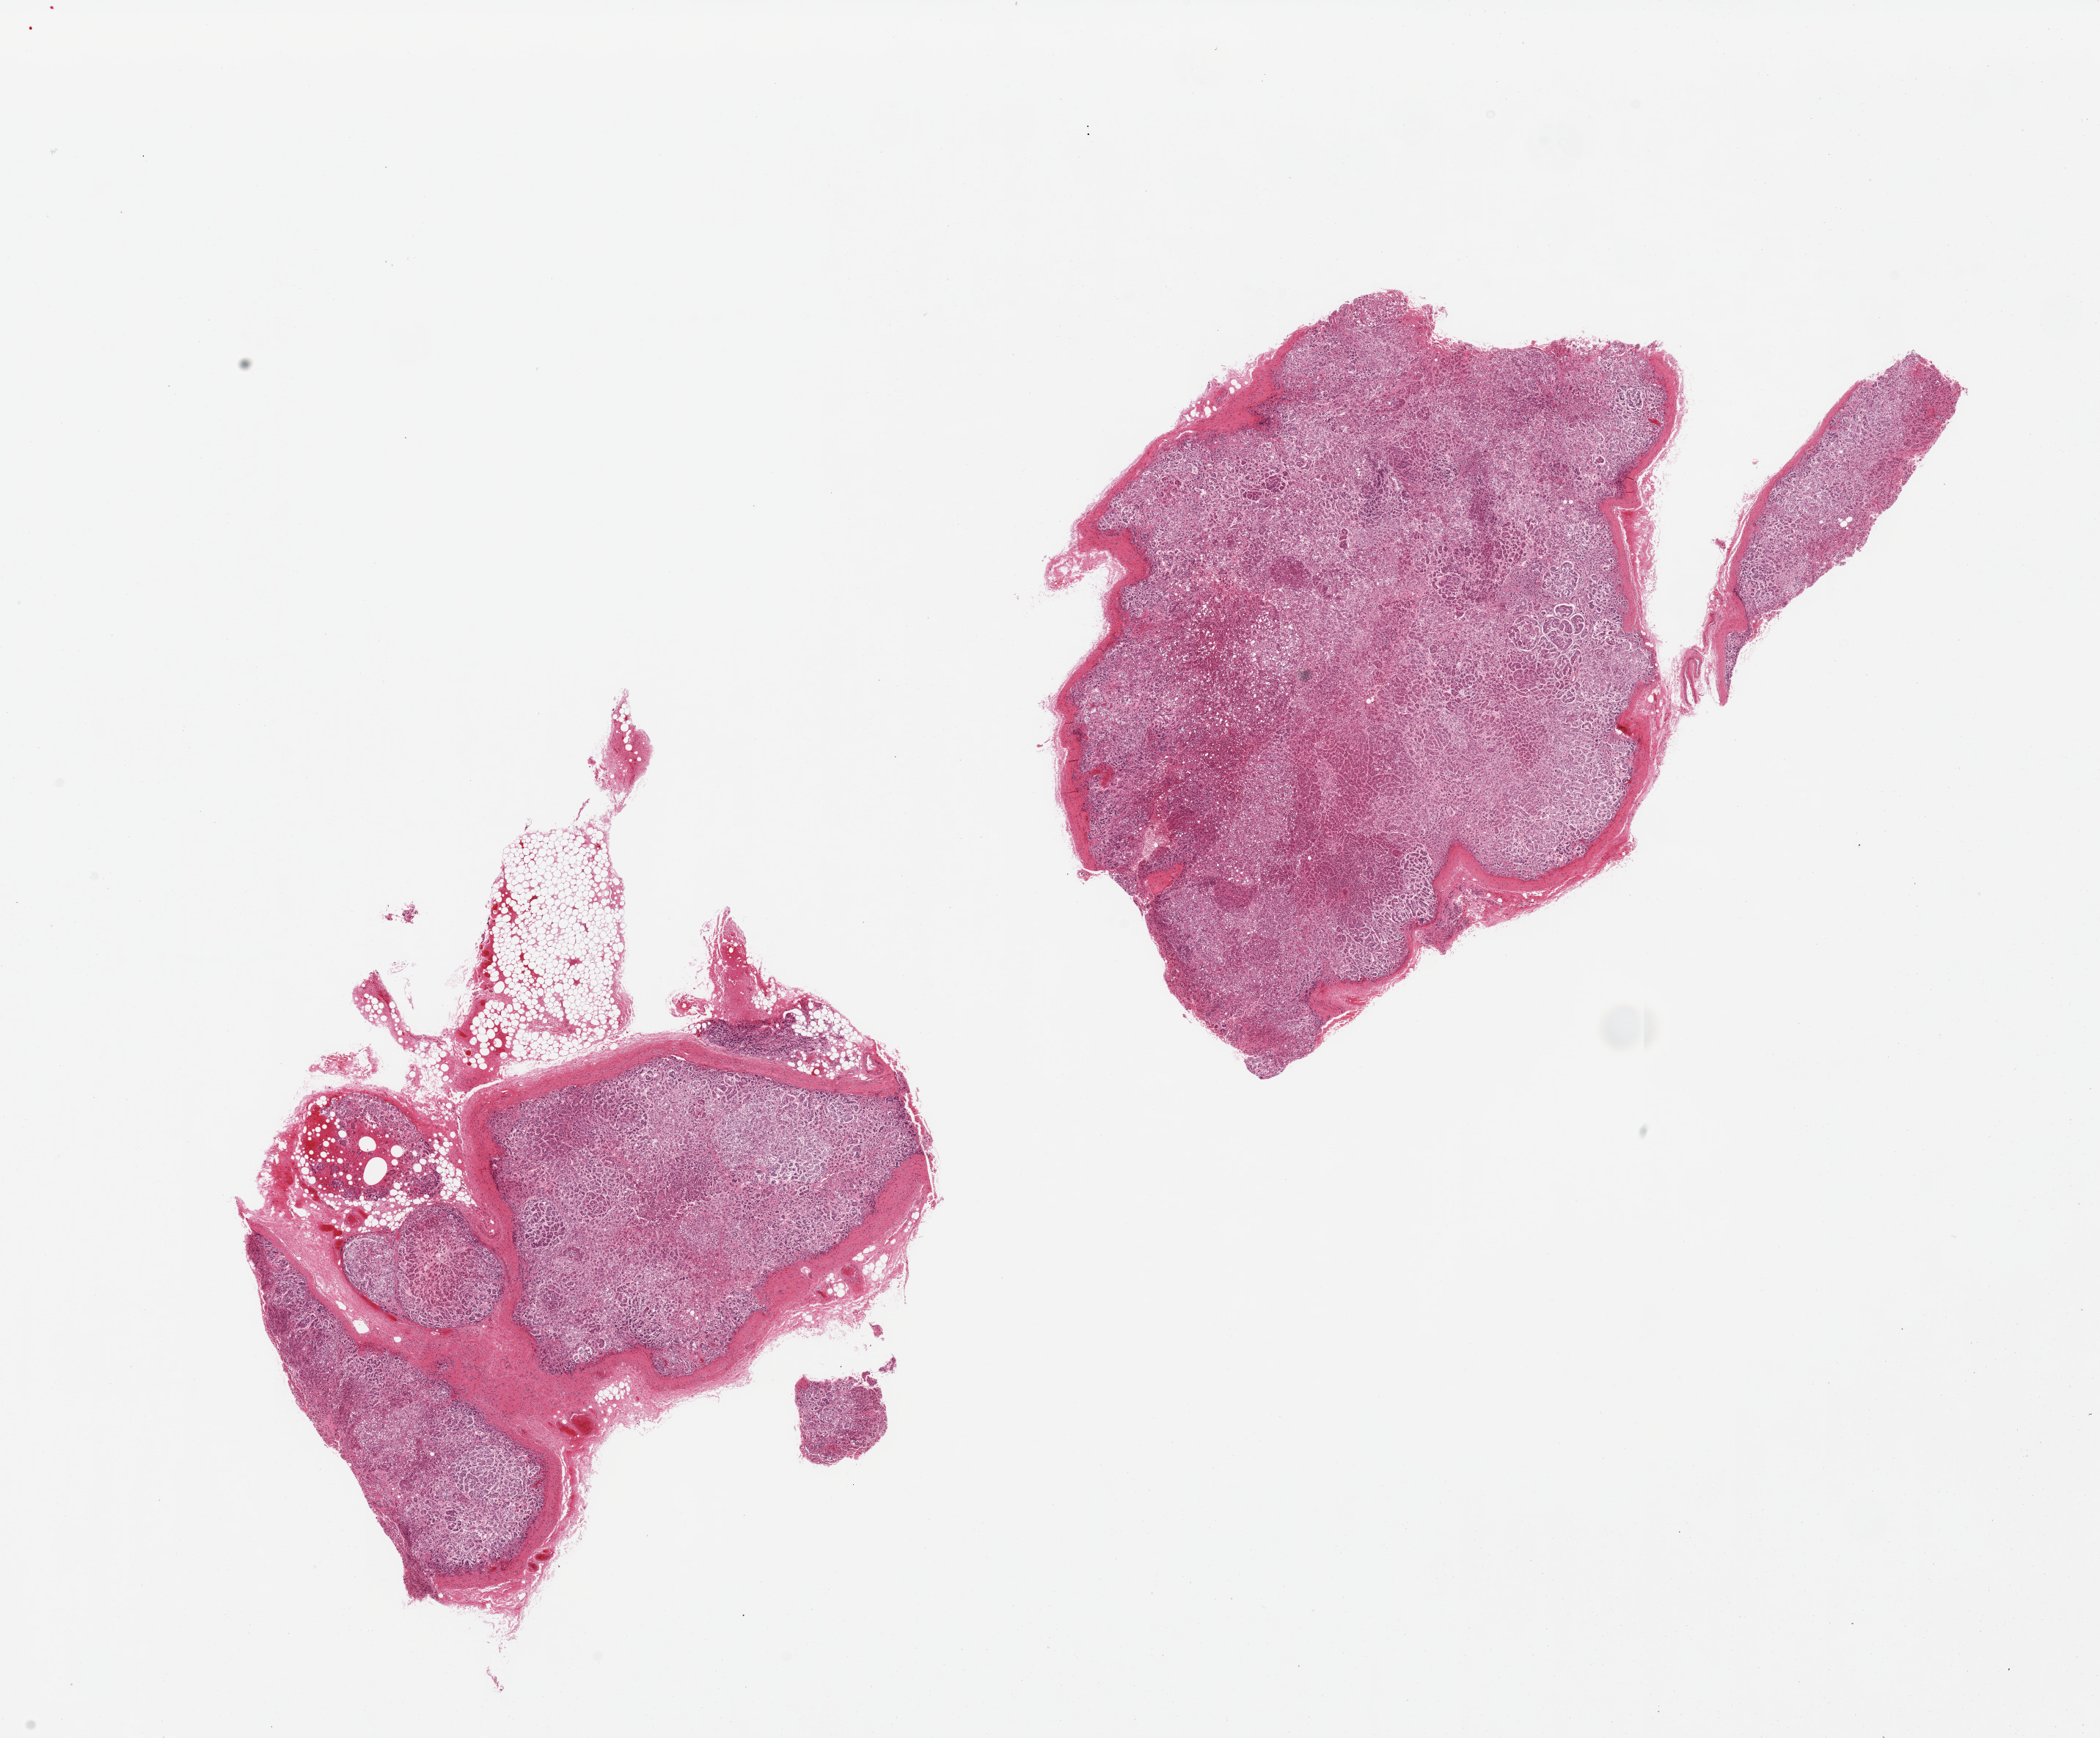
Whole-slide image, H&E stain — low-resolution overview of the scanned area, about 22.6 x 18.7 mm (from a 20x scan), PAXgene-fixed, paraffin-embedded tissue, sampled site (target tissue): adrenal gland, tissue donor sample. Female donor.
Review note (as recorded): 2 pieces, all cortex, badly autolyzed, focal adherent fat.